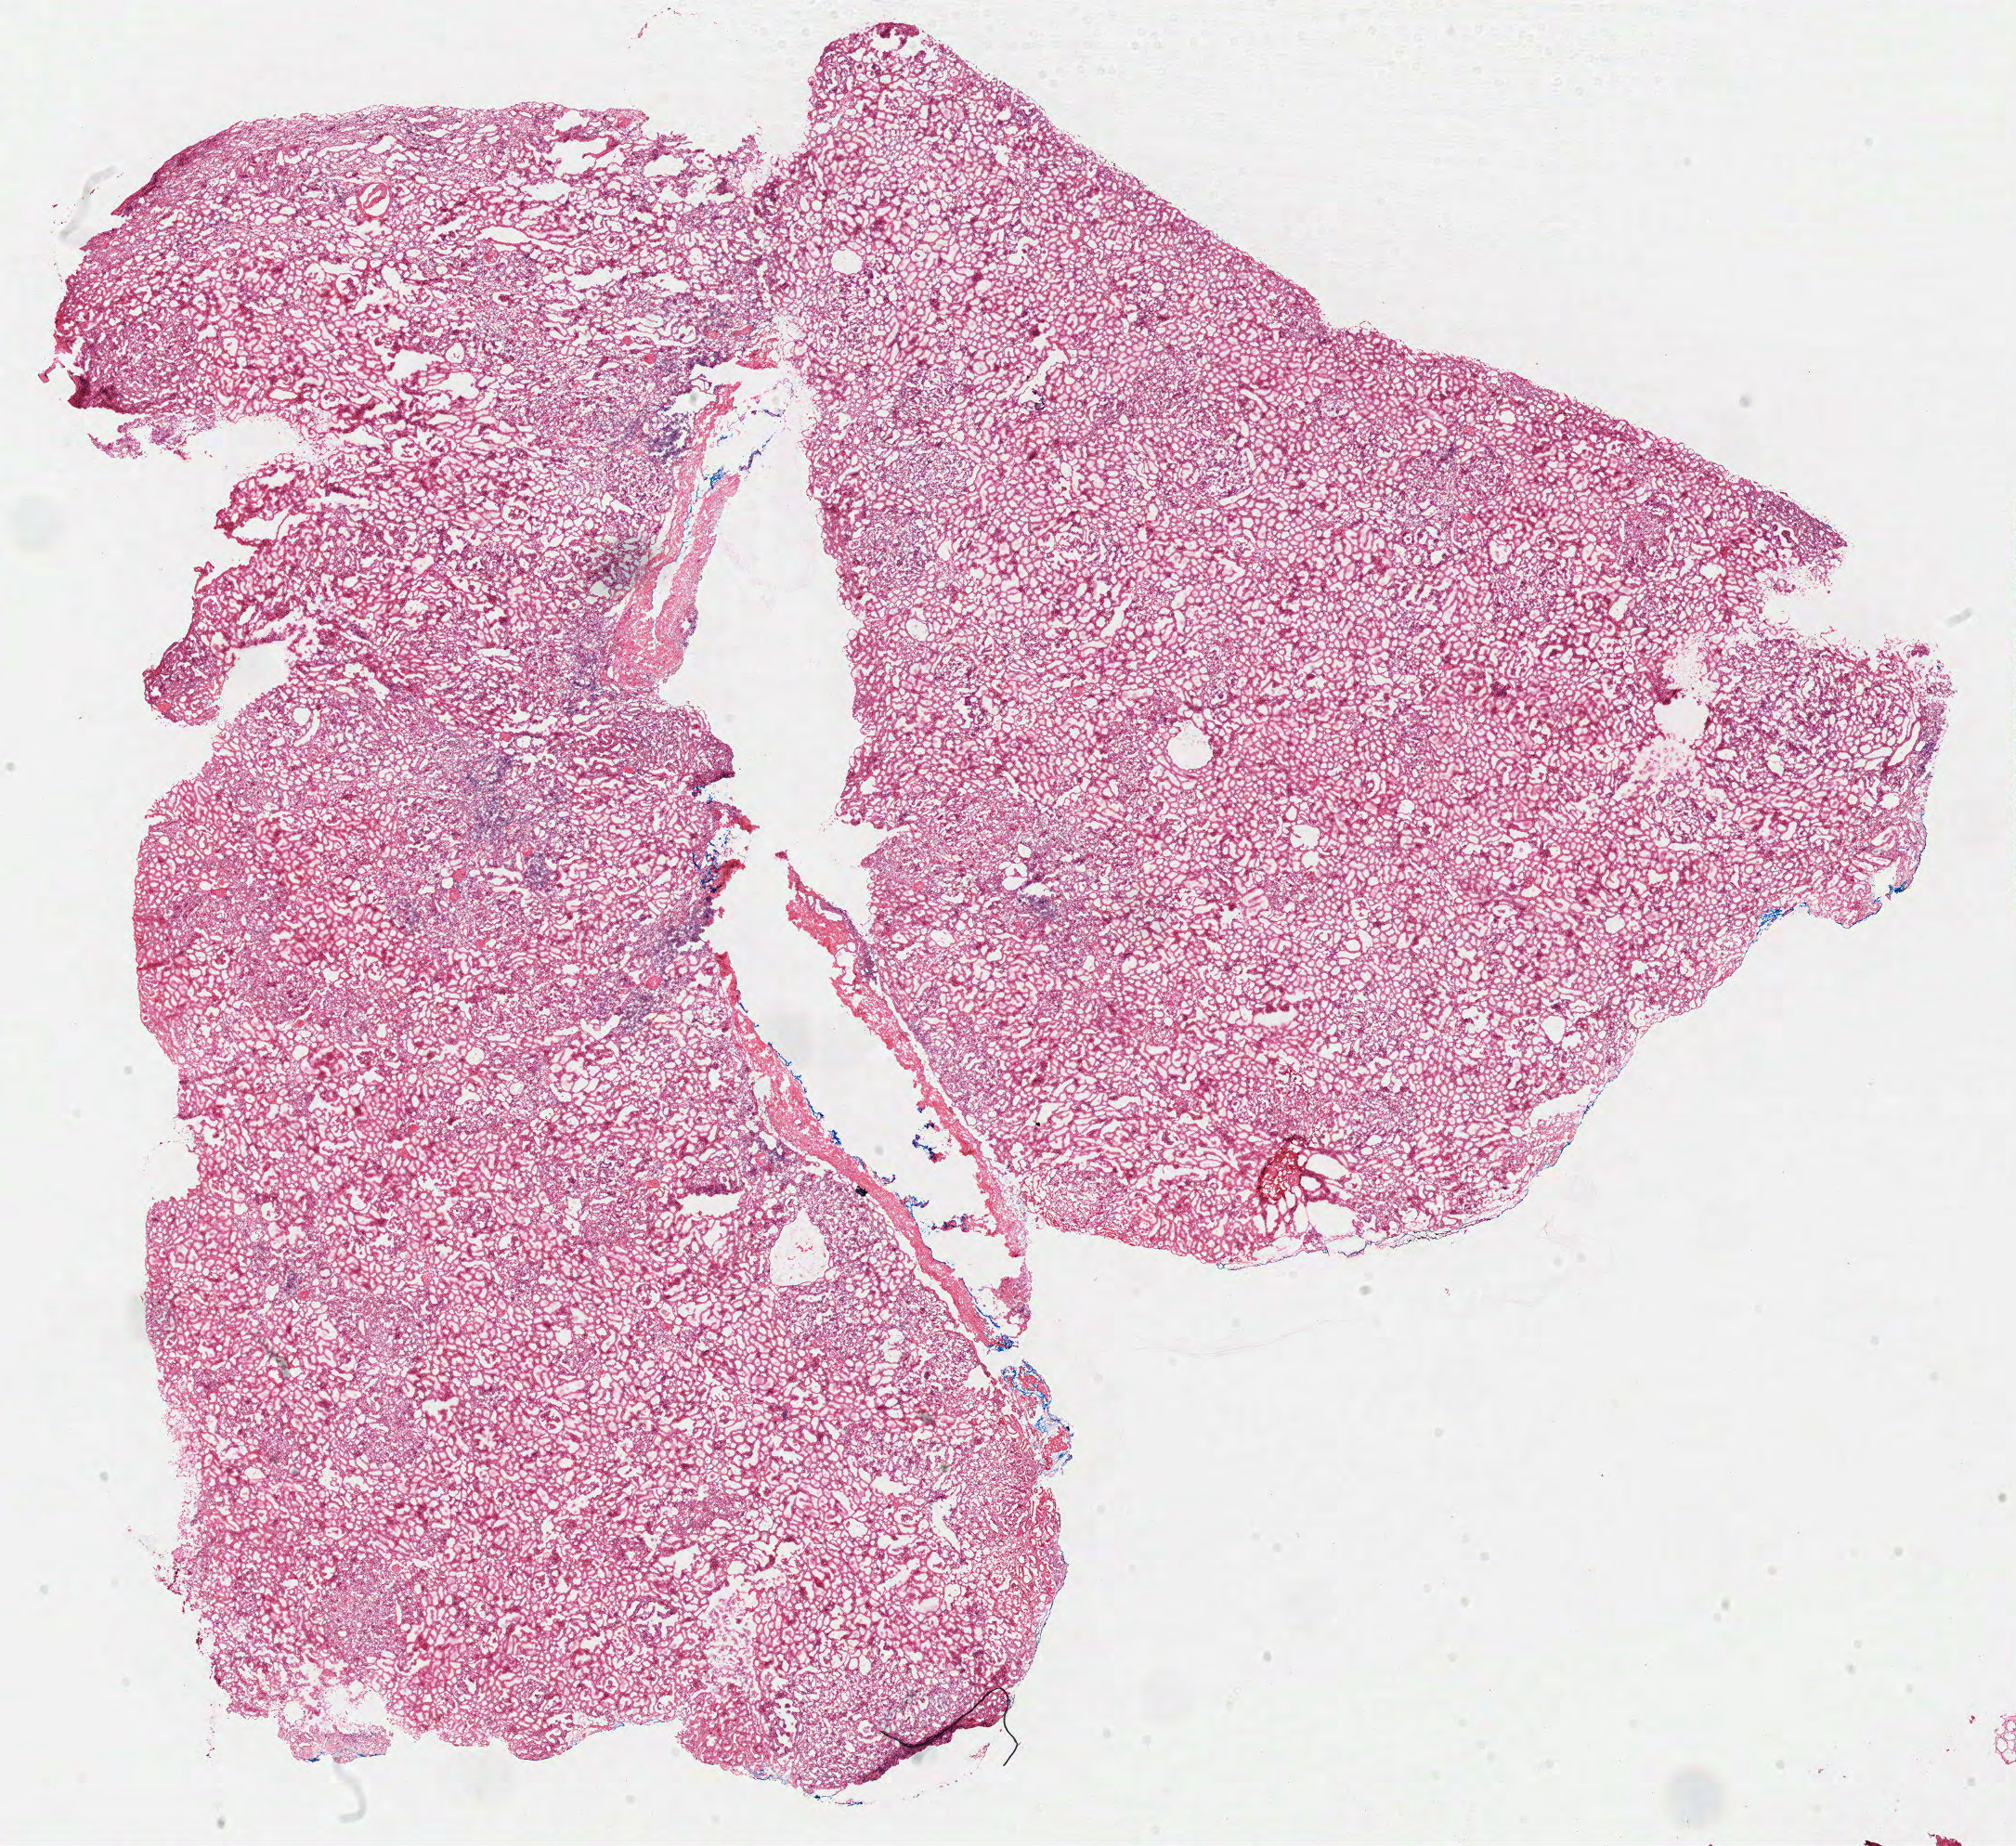
Digitized H&E-stained tissue section (whole slide), whole scanned area (about 17.1 x 15.7 mm) shown as a low-resolution overview, frozen section from the top of the tissue portion, sample: solid tissue normal (non-tumour tissue), kidney. Patient: female, age at initial diagnosis 74 years.
This section: solid tissue normal (non-tumour) sample from the same patient. Patient diagnosis: Papillary adenocarcinoma, NOS.